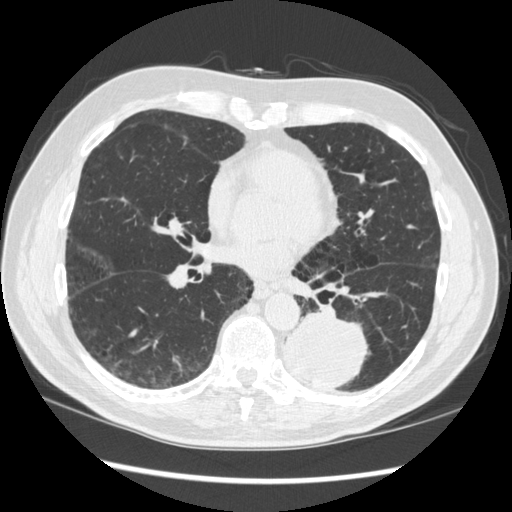
Chest CT (low-dose screening protocol), one axial image; baseline annual screen; lung window (W 1500 / L -600 HU); standard (soft-tissue) reconstruction kernel (STANDARD); slice 149 of 348 in the series; 512 × 512 image matrix, field of view 360 × 360 mm. Male participant, aged 72 years at enrolment. Current smoker at enrolment.
Expert-annotated lung lesion, bounding box <268,302,372,393> (left, top, right, bottom; pixels). The screening reader recorded 2 non-calcified nodules or masses ≥4 mm on this exam; which of them this box marks is not recorded. Lung cancer was diagnosed 37 days after this screen: squamous cell carcinoma, NOS, left lower lobe, stage IIIA (AJCC 6th edition), 60 mm at pathology.